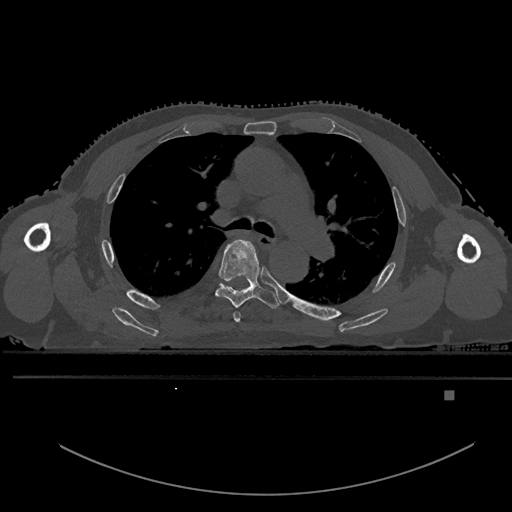
CT including the spine, one axial slice; slice 362 of 969 in the series (ordered by position); bone window (W 1800 / L 400 HU); 0.5 mm slice thickness; 512 × 512 image matrix, field of view 456 × 456 mm. Patient: male, 82 years. Case-level facts recorded for this patient, not image findings: primary cancer: prostate.
Annotated regions visible in this slice (semi-automatic segmentation, software-assisted and operator-edited):
- T4 vertebra: bounding box (x1, y1, x2, y2) in pixels: (233, 312, 240, 323)
- T5 vertebra: (215, 239, 280, 309)